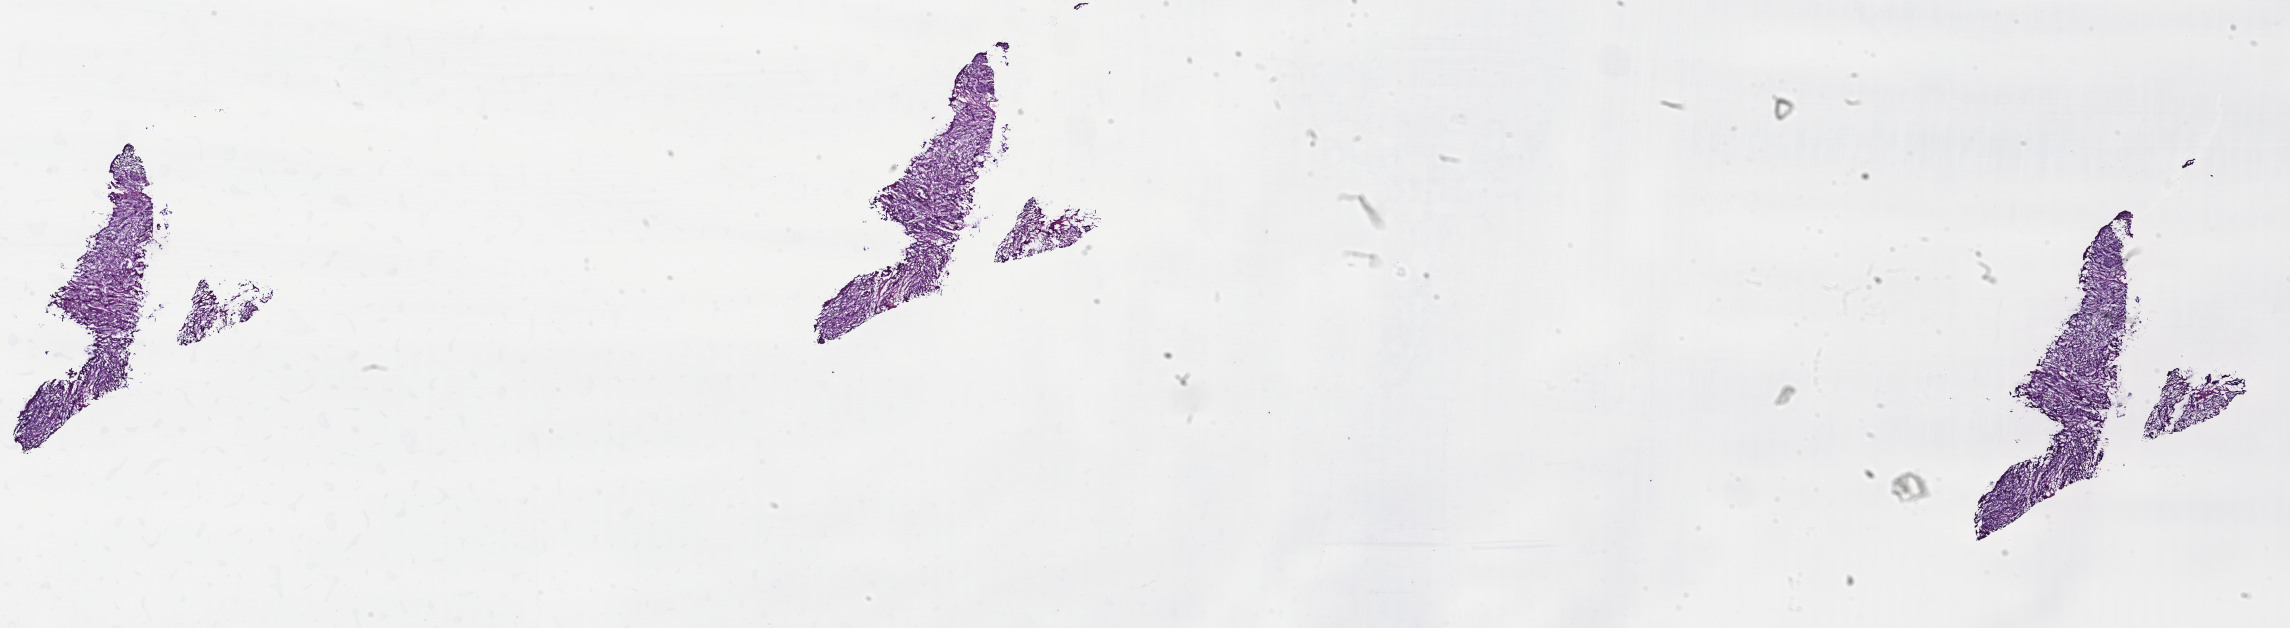
Whole-slide histology image, H&E, whole scanned area (about 36.0 x 9.9 mm, from a 40x scan) shown as a low-resolution overview. Frozen section from the top of the tissue portion. Head and neck, primary tumour sample. Male, age 78 years at initial diagnosis. Pathologist review of this section (percent, as recorded): tumour cells 75%, tumour nuclei 75%.
Histologic diagnosis: Squamous cell carcinoma, NOS.